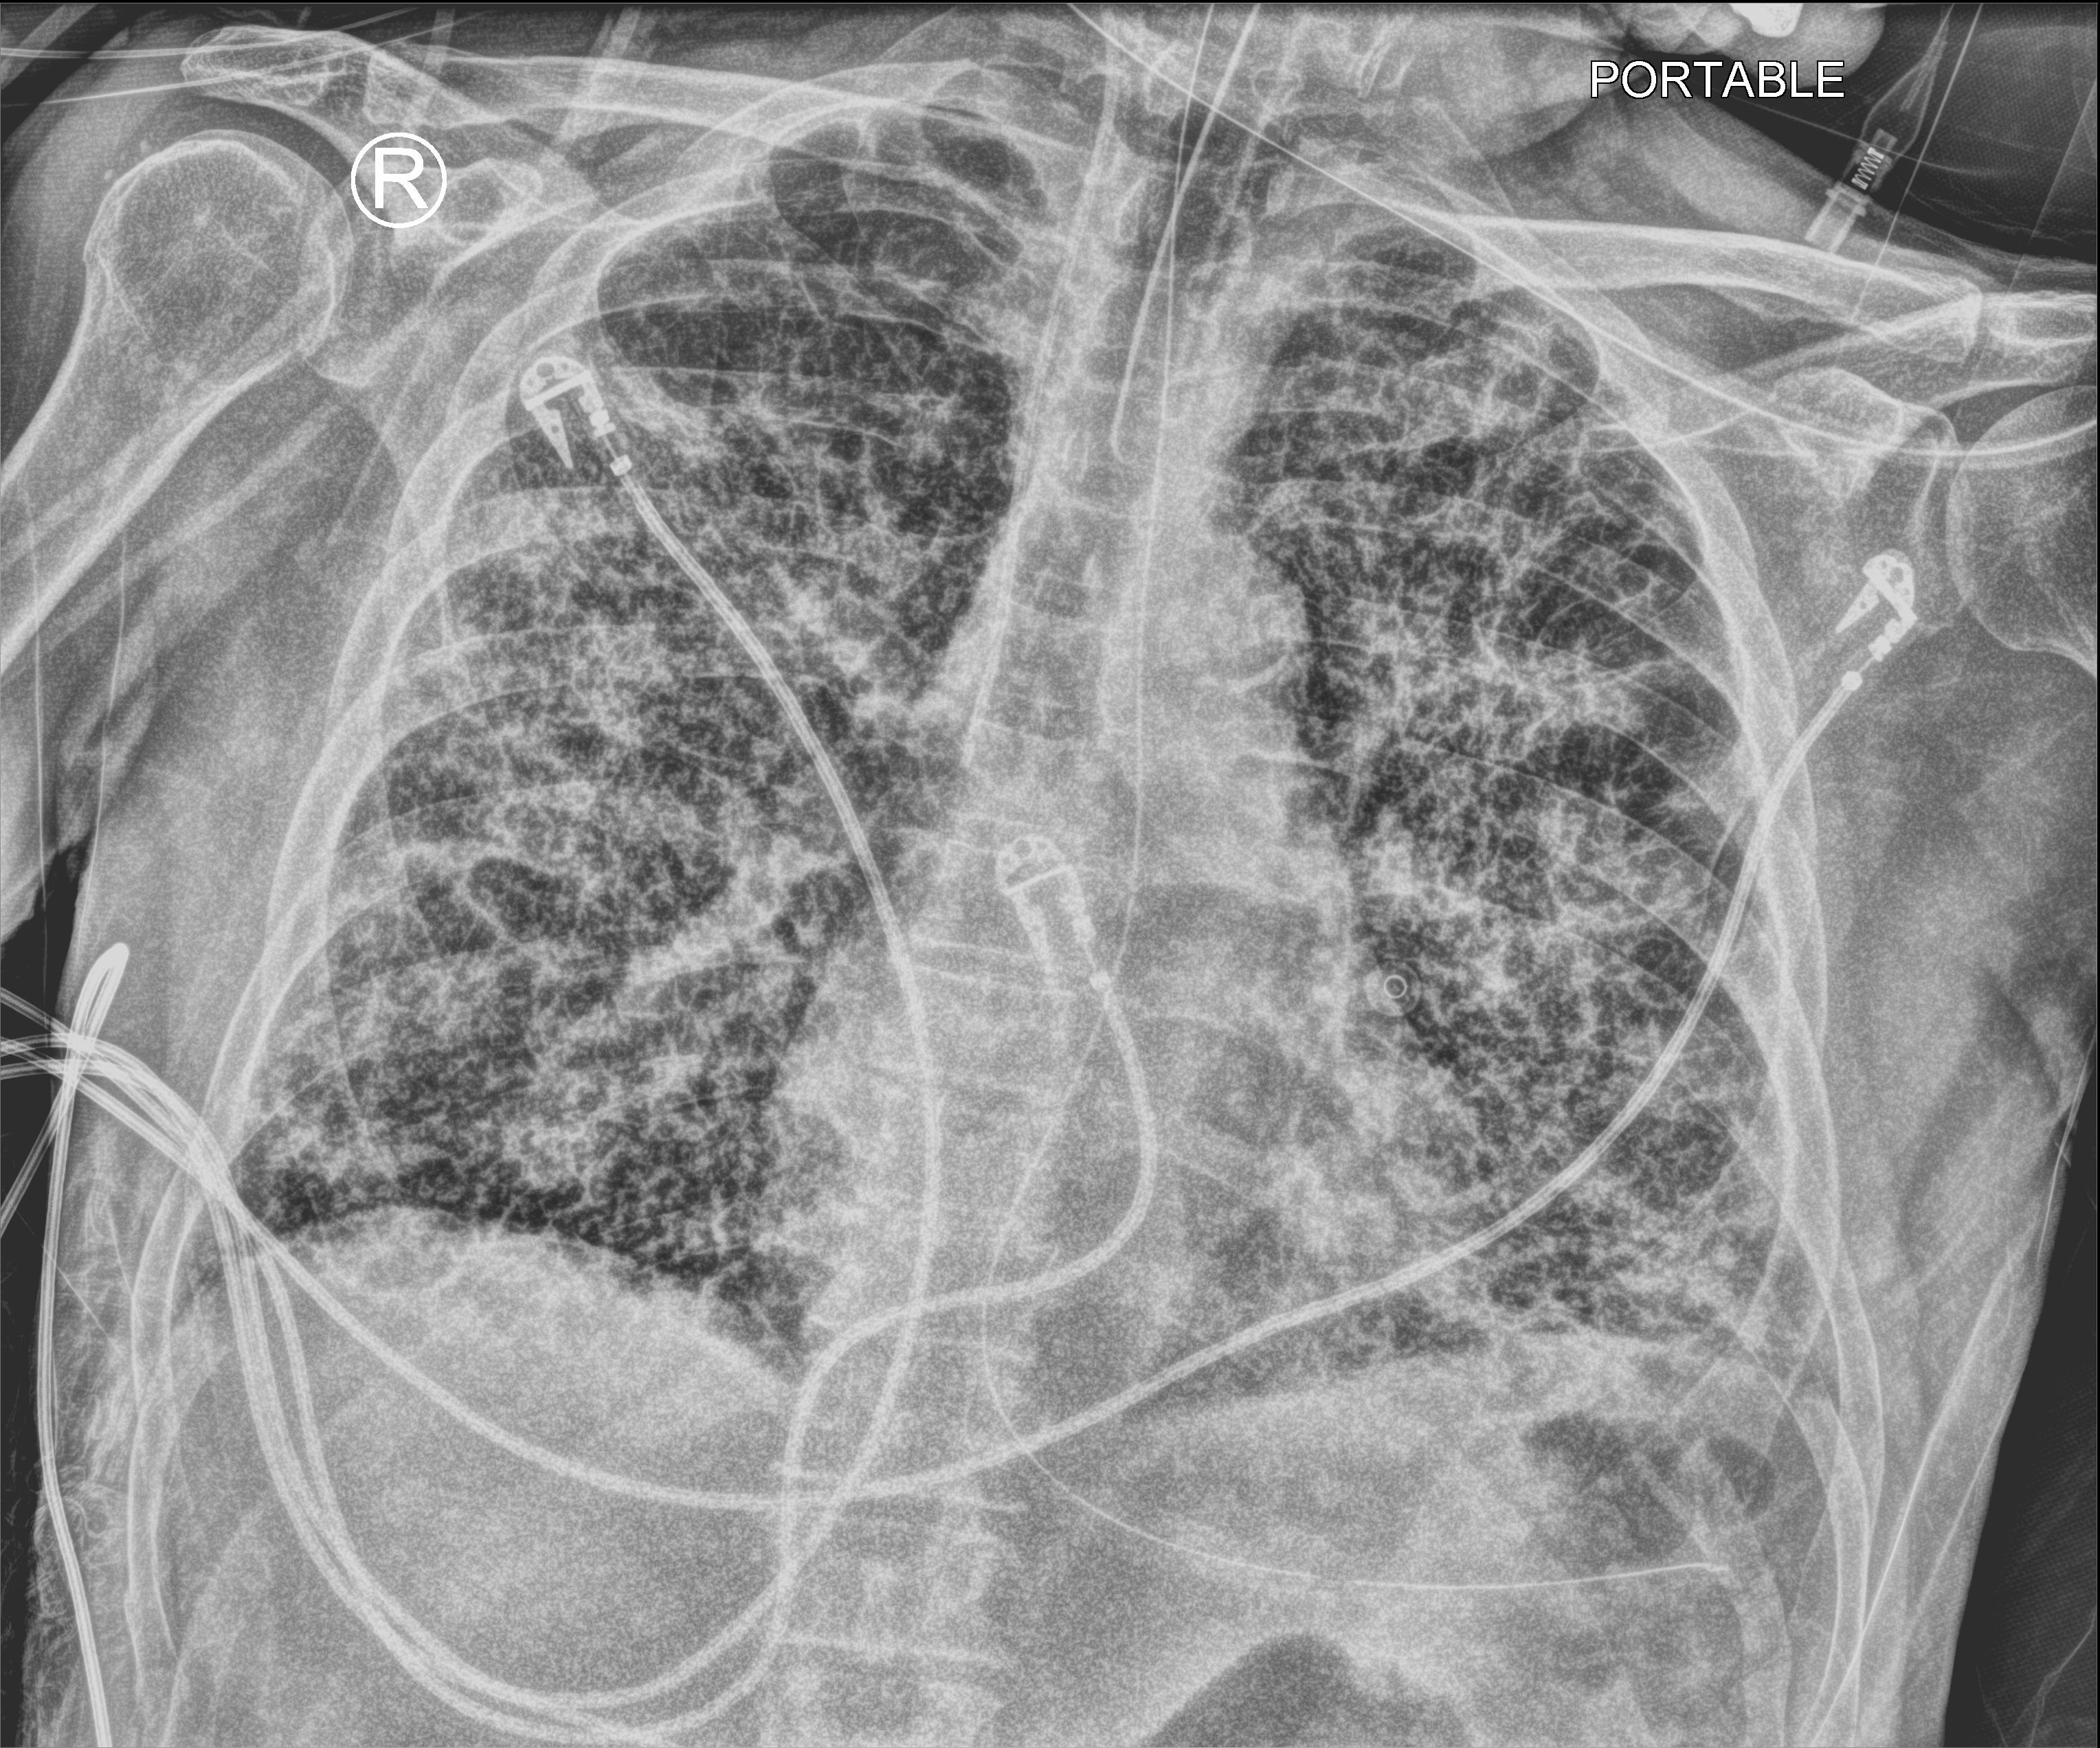
Bedside chest radiograph (computed radiography), anteroposterior (AP) projection. Patient hospitalised with COVID-19; male, aged 75–90 years.
Admission-level facts for this patient (not findings on this image; timing relative to this image not recorded): other chronic lung disease (admission record): yes; hypertension (admission record): yes.